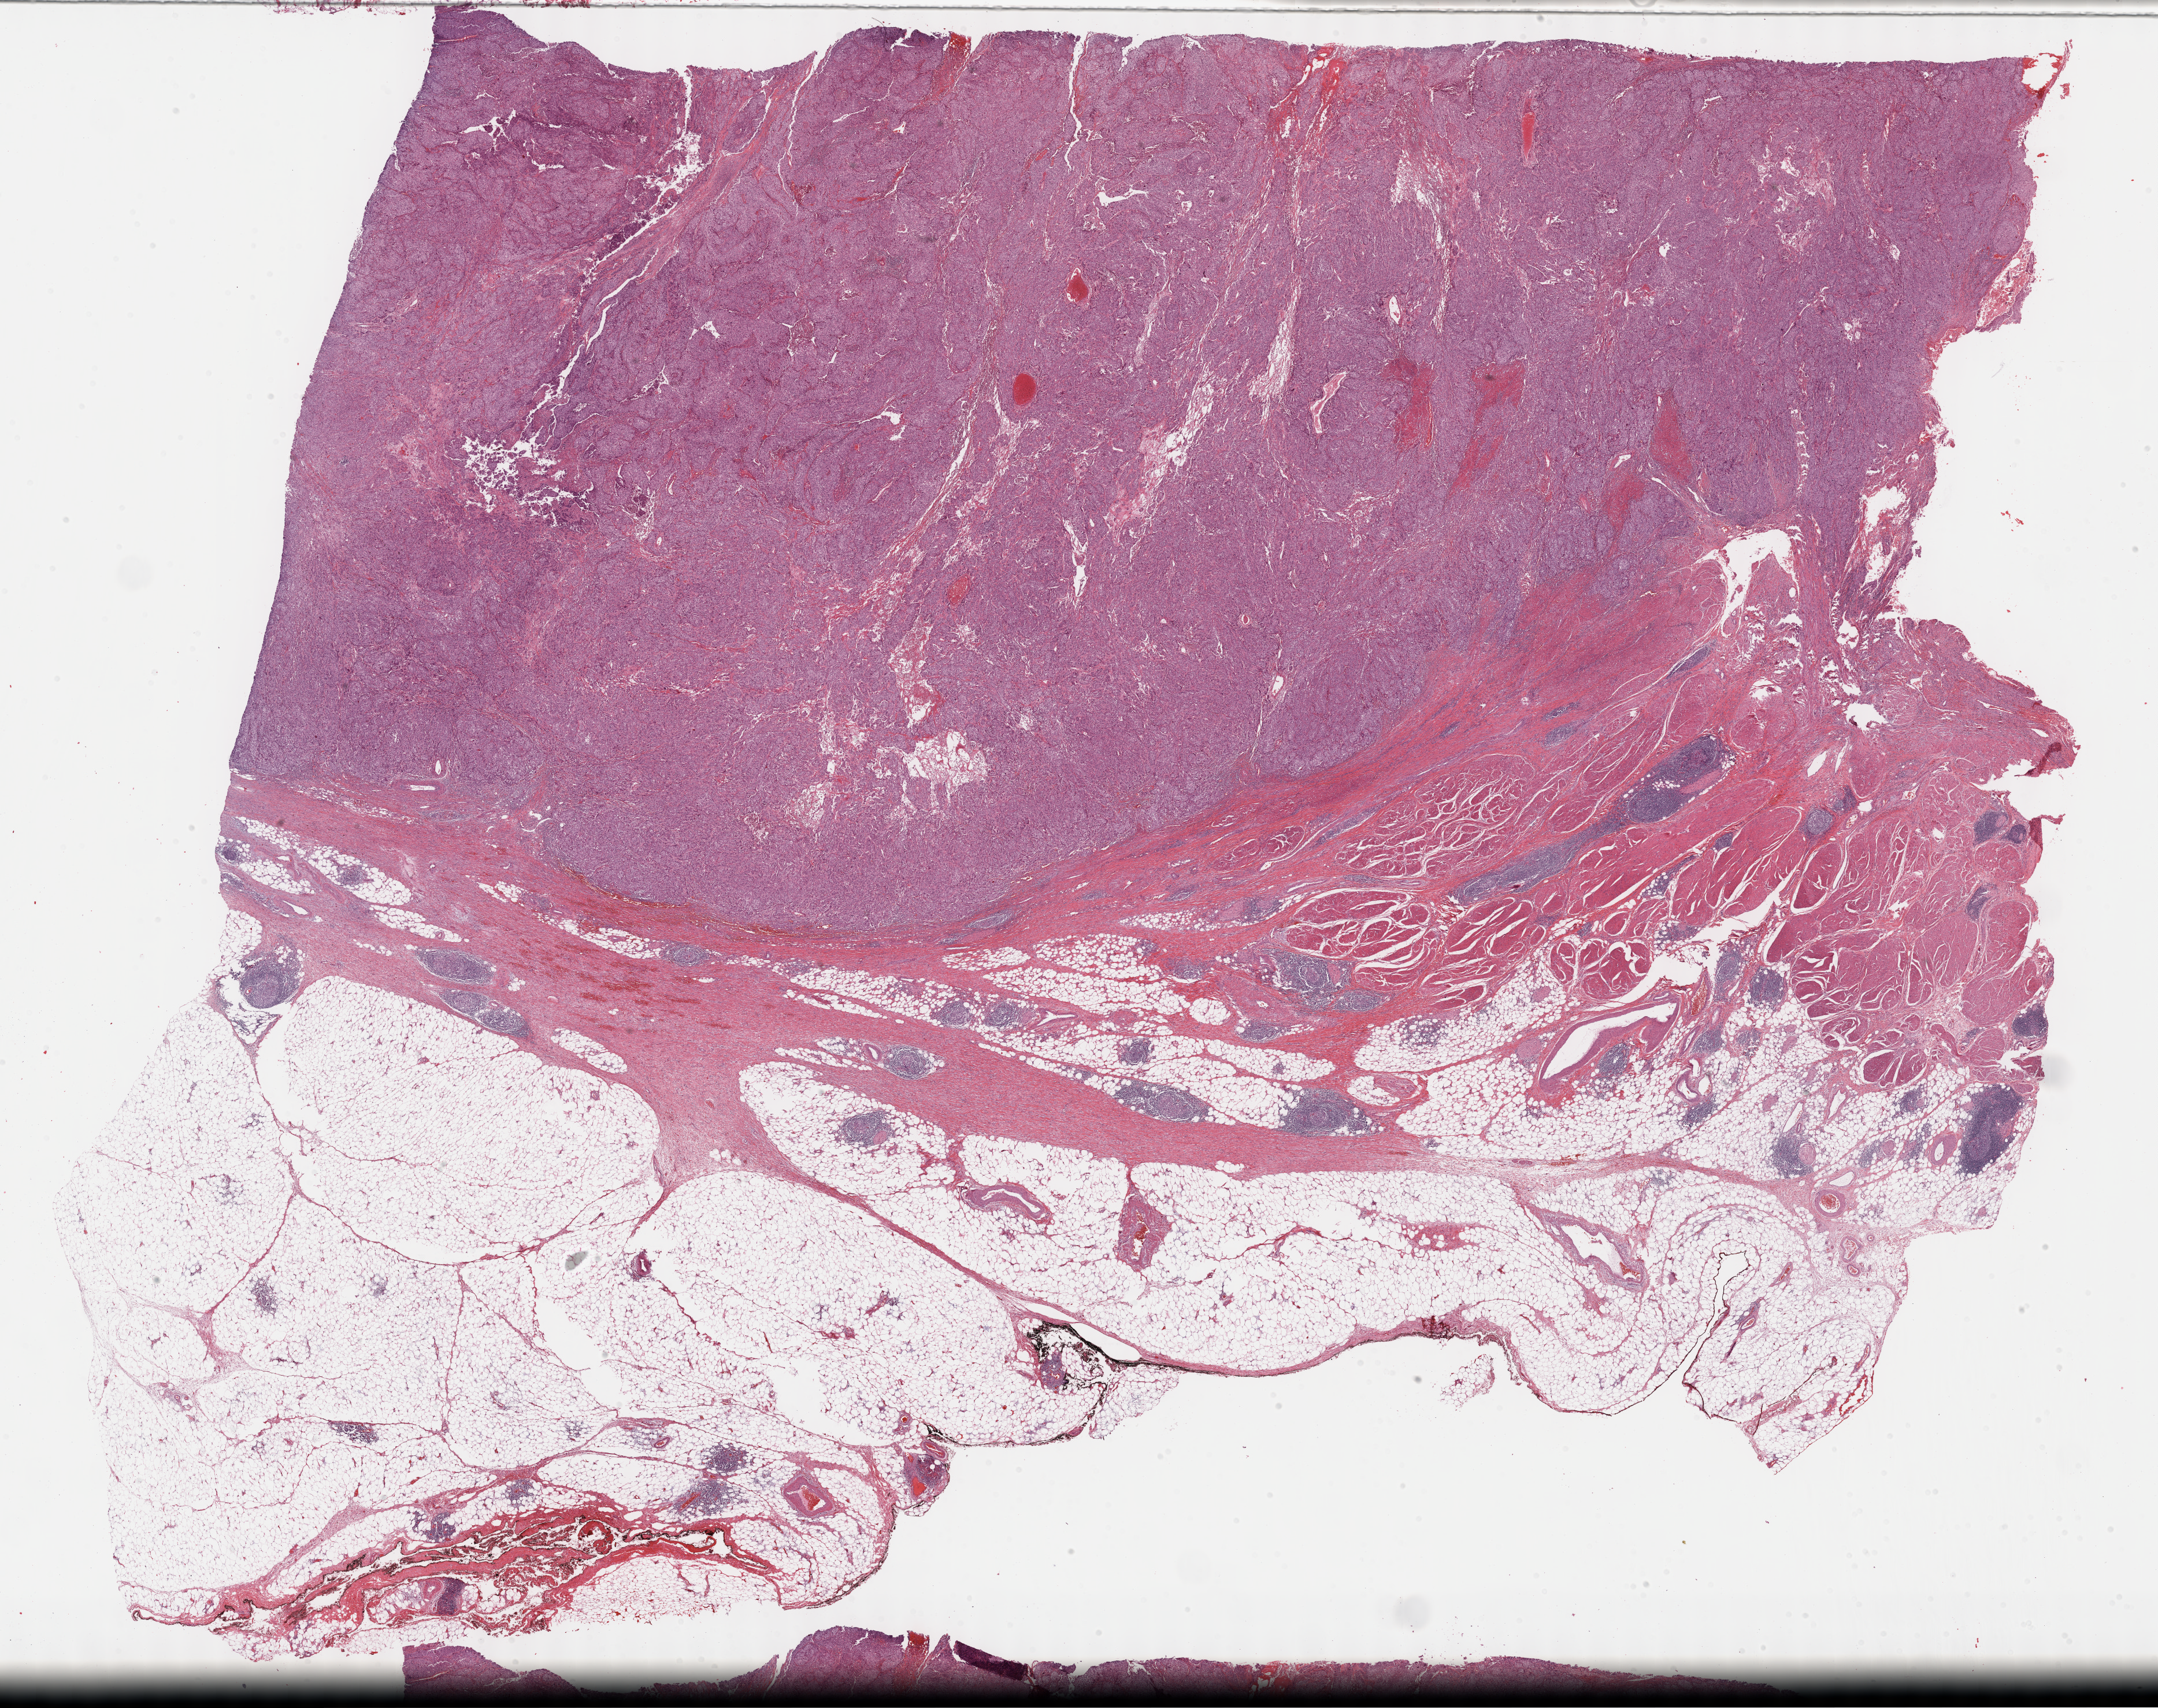
Hematoxylin and eosin (H&E) stained whole-slide image — a low-resolution overview of the entire scanned area, about 30.2 x 23.9 mm (acquisition: 40x scan); formalin-fixed paraffin-embedded (FFPE) diagnostic section; primary tumour sample from the bladder. Female, age 88 years at initial diagnosis. Histologic grade: high grade.
AJCC pathologic stage: III (6th edition). Lymph nodes positive (case pathology): 0 of 48 examined. Histologic diagnosis: Papillary transitional cell carcinoma.